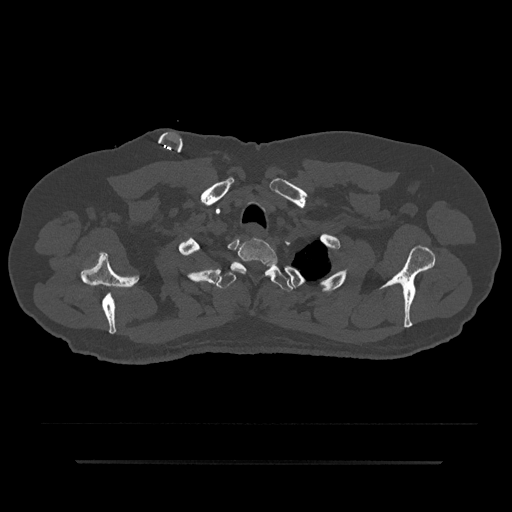
CT including the spine, one axial slice; slice 717 of 797 in the series (ordered by position); reconstruction kernel Br40s/3; 120 kVp; bone window (W 1800 / L 400 HU); 0.5 mm slice thickness; 512 × 512 image matrix, field of view 464 × 464 mm. Male patient, age 59 years. From the clinical record (not read from this slice): primary cancer: bile ducts; vertebrae with lytic lesions (as recorded): T10.
Outlined on this slice (semi-automatic segmentation, software-assisted and operator-edited):
- T1 vertebra: box from (x=231, y=238) to (x=278, y=276) px
- T2 vertebra: (x=215, y=263)–(x=293, y=292)